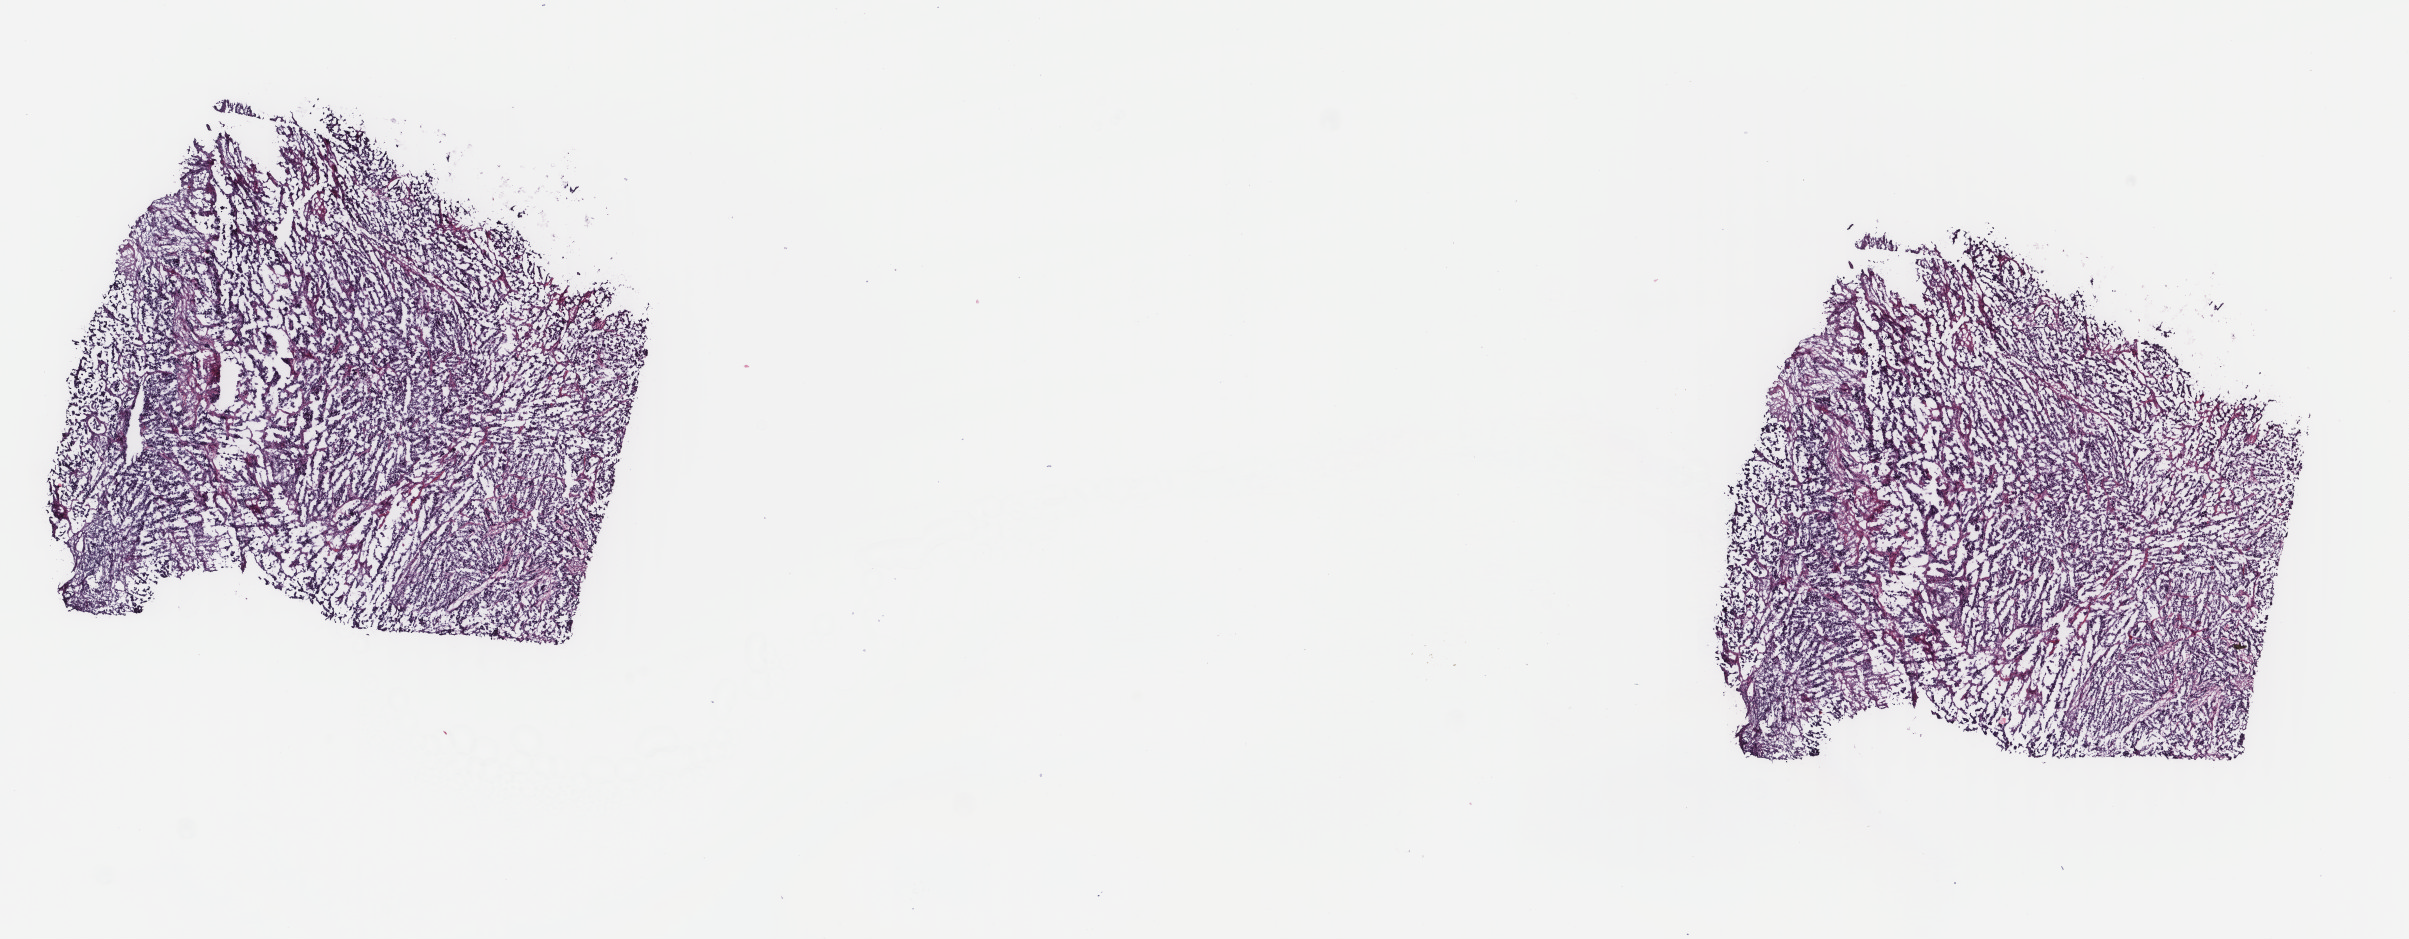
Digitized Hematoxylin and eosin (H&E) stained tissue section (whole slide) — a low-resolution overview of the entire scanned area, about 19.1 x 7.5 mm; frozen section; sample: primary tumour, cervix. Female patient; age at initial diagnosis 60 years. Histologic grade: G3 (poorly differentiated). Pathologist review of this section (percent, as recorded): tumour cells 100%, tumour nuclei 80%, normal cells 0%, stromal cells 0%, necrosis 0%. Infiltration values recorded for this section: lymphocyte infiltration 0%, monocyte infiltration 0%, neutrophil infiltration 0%.
- lymph nodes positive (case pathology): 0 of 18 examined
- FIGO stage: IB1
- histologic diagnosis: Adenocarcinoma, endocervical type (cervix uteri)